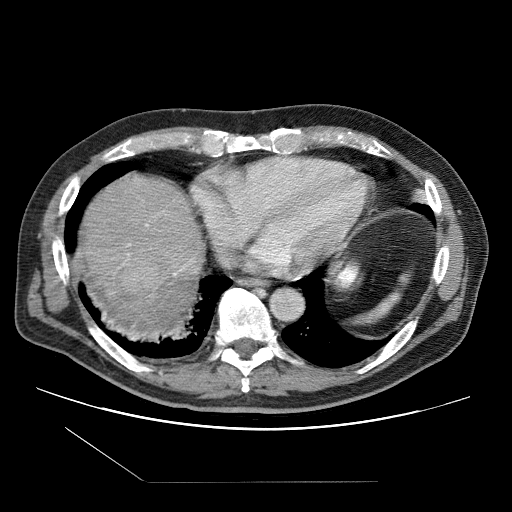
Contrast-enhanced abdominal CT (liver protocol), one axial slice; one of 2 acquisitions stored at this slice position; soft-tissue window (W 400 / L 40 HU); 512 × 512 image matrix. Case-level facts recorded for this patient, not image findings: diagnosis: hepatocellular carcinoma (patient treated with transarterial chemoembolisation; whether this scan precedes or follows treatment is not stated here); TNM stage (as recorded): Stage-IIIB; Child-Pugh class: A; tumour differentiation: well differentiated; tumour nodularity: multinodular.
Structures marked on this image (semi-automatic segmentation, software-assisted and operator-edited):
- liver parenchyma outside the tumour (the mass and vessels are separate outlines, so this box may not span the whole liver): box from (x=76, y=176) to (x=204, y=336) px
- mass: (x=82, y=243)–(x=164, y=294)
- liver vessels: (x=128, y=224)–(x=176, y=275)